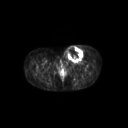
FDG PET of an extremity soft-tissue mass (from a PET/CT study), one axial slice. Position 54 of 267 along the scan axis. 128 × 128 image matrix, field of view 600 × 600 mm. Patient: female, 24 years. From the clinical record (not read from this slice): histological type: leiomyosarcoma; grade: high; site of the primary tumour: groin.
Outlined on this slice (expert contour drawn on MRI and transferred to this co-registered scan by the dataset authors):
- gross tumour volume including surrounding oedema: bounding box <63,44,87,62> (left, top, right, bottom; pixels)
- gross tumour volume (mass): <66,45,84,62>